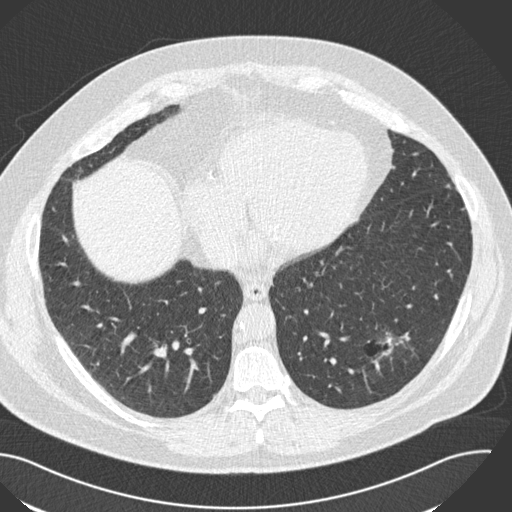
Low-dose screening chest CT, one axial slice. Position 64 of 153 along the scan axis. Reconstruction kernel B30f. 120 kVp. Lung window (W 1500 / L -600 HU). 2 mm slice thickness. 512 × 512 image matrix.
Structures marked on this image (outlined manually by an expert reader):
- lesion 1 (tumor, lower lobe of left lung): box from (x=386, y=336) to (x=404, y=348) px